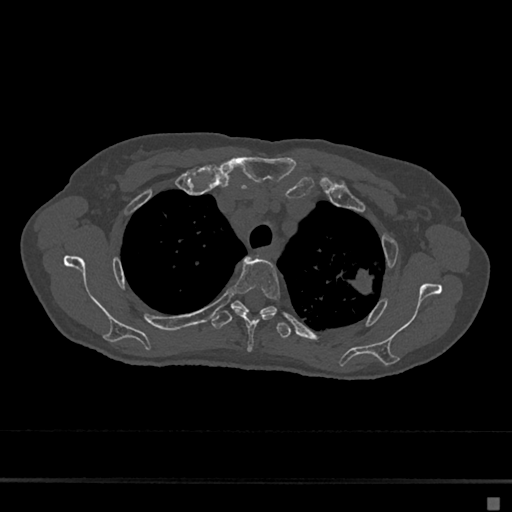
CT including the spine, one axial slice; slice 528 of 797 in the series (ordered by position); 120 kVp; bone window (W 1800 / L 400 HU); 0.5 mm slice thickness; 512 × 512 image matrix, field of view 360 × 360 mm. Patient: female, 68 years. Case-level facts recorded for this patient, not image findings: primary cancer: renal.
Outlined on this slice (semi-automatic segmentation, software-assisted and operator-edited):
- T3 vertebra: bounding box [x1, y1, x2, y2] px = [231, 257, 280, 351]
- T4 vertebra: [211, 301, 291, 339]